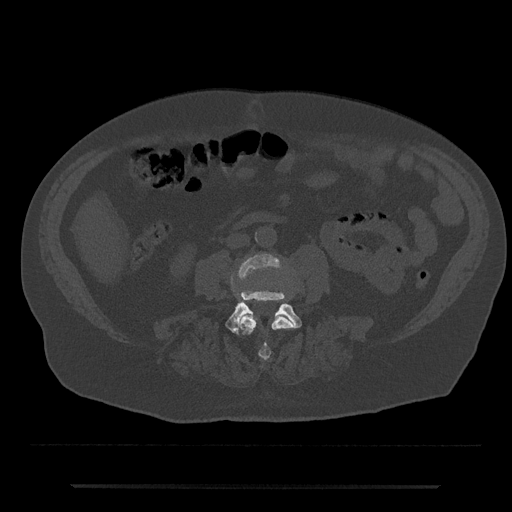
CT including the spine, one axial slice. Slice 376 of 797 in the series (ordered by position). 120 kVp. Bone window (W 1800 / L 400 HU). 0.5 mm slice thickness. 512 × 512 image matrix, field of view 434 × 434 mm. Patient: male, 80 years. Case-level facts recorded for this patient, not image findings: primary cancer: prostate; vertebrae with lytic lesions (as recorded): L1, T11.
Annotated regions visible in this slice (semi-automatic segmentation, software-assisted and operator-edited):
- L3 vertebra: box from (x=231, y=254) to (x=294, y=360) px
- L4 vertebra: (x=225, y=291)–(x=302, y=335)